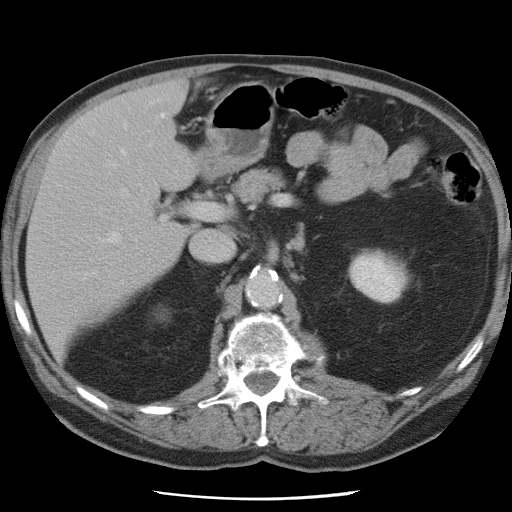
Contrast-enhanced abdominal CT, one axial slice; position 42 of 78 along the scan axis; 120 kVp; intravenous contrast given; soft-tissue window (W 400 / L 40 HU); 512 × 512 image matrix. Male patient, age 75 years. Case-level facts recorded for this patient, not image findings: diagnosis: colorectal cancer liver metastases, imaged before liver resection; multiple liver metastases: yes; largest metastasis: 2.4 cm.
Structures marked on this image (expert manual segmentation):
- hepatic veins: bounding box <98,125,129,242> (left, top, right, bottom; pixels)
- liver: <29,82,197,351>
- planned liver remnant (the part of the liver to remain after resection): <29,120,186,350>
- portal vein (with intrahepatic branches): <121,189,195,214>